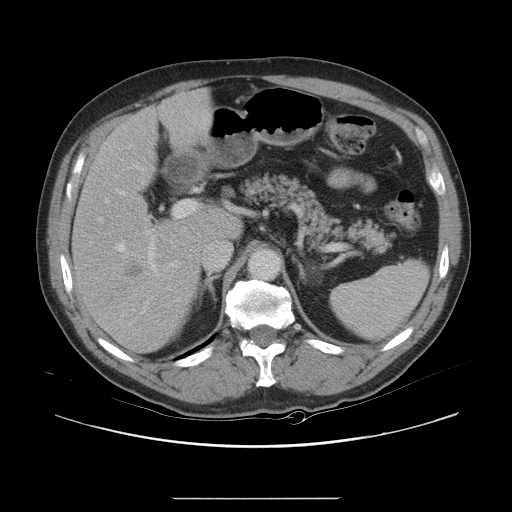
Contrast-enhanced abdominal CT, one axial slice. Slice 15 of 40 in the series (ordered by position). 120 kVp. Soft-tissue window (W 400 / L 40 HU). 512 × 512 image matrix. Male patient, age 64 years. From the clinical record (not read from this slice): diagnosis: colorectal cancer liver metastases, imaged before liver resection; multiple liver metastases: yes; largest metastasis: 3.2 cm; chemotherapy before resection: yes.
Structures marked on this image (outlined manually by an expert reader):
- hepatic veins: bounding box [x1, y1, x2, y2] px = [116, 182, 145, 252]
- liver: [74, 93, 239, 352]
- planned liver remnant (the part of the liver to remain after resection): [89, 93, 239, 241]
- portal vein (with intrahepatic branches): [149, 202, 195, 270]
- liver metastasis: [108, 263, 145, 301]